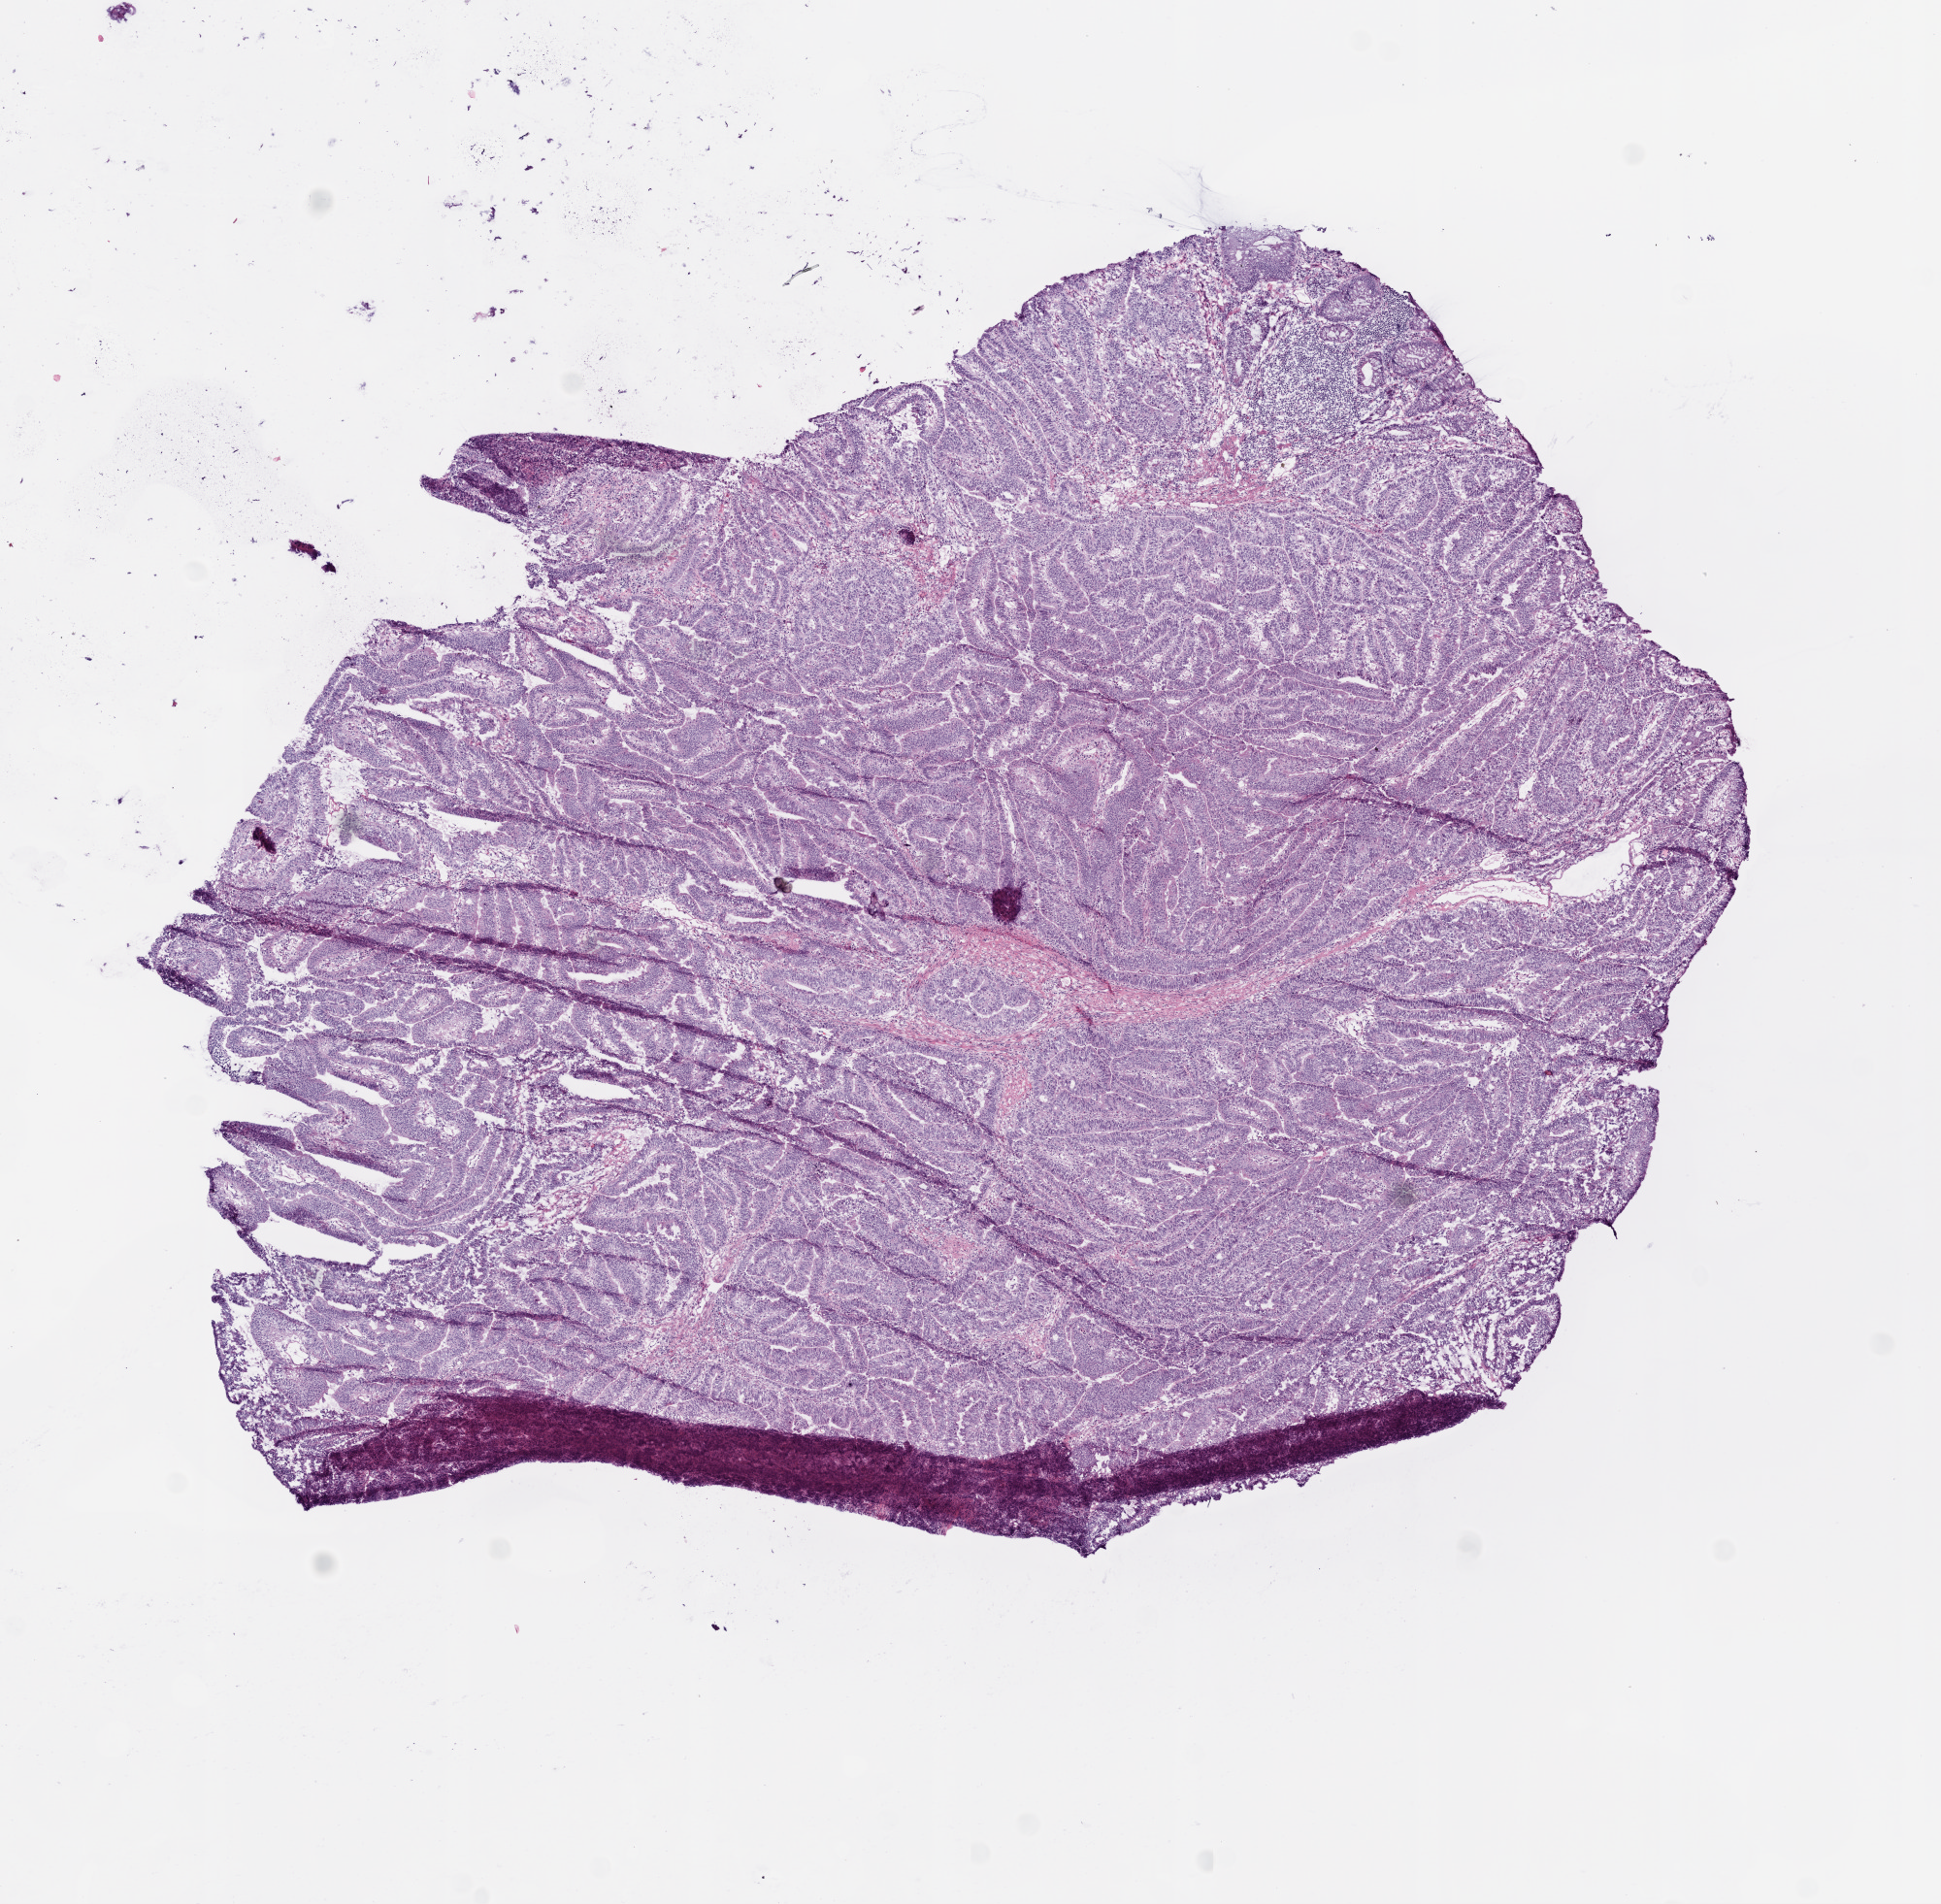
Digitized Hematoxylin and eosin (H&E) stained tissue section (whole slide) — whole scanned area (about 8.0 x 7.9 mm) shown as a low-resolution overview, frozen section from the top of the tissue portion, sample: primary tumour, rectum. Male patient; age at initial diagnosis 62 years. Slide review estimates, as recorded: tumour cells 85%, tumour nuclei 85%, normal cells 10%, stromal cells 5%, necrosis 0%.
• TNM: T3 N2 M0
• histologic diagnosis: Adenocarcinoma, NOS (rectosigmoid junction)
• AJCC pathologic stage: IIIC (6th edition)
• lymph nodes positive (case pathology): 31 of 45 examined